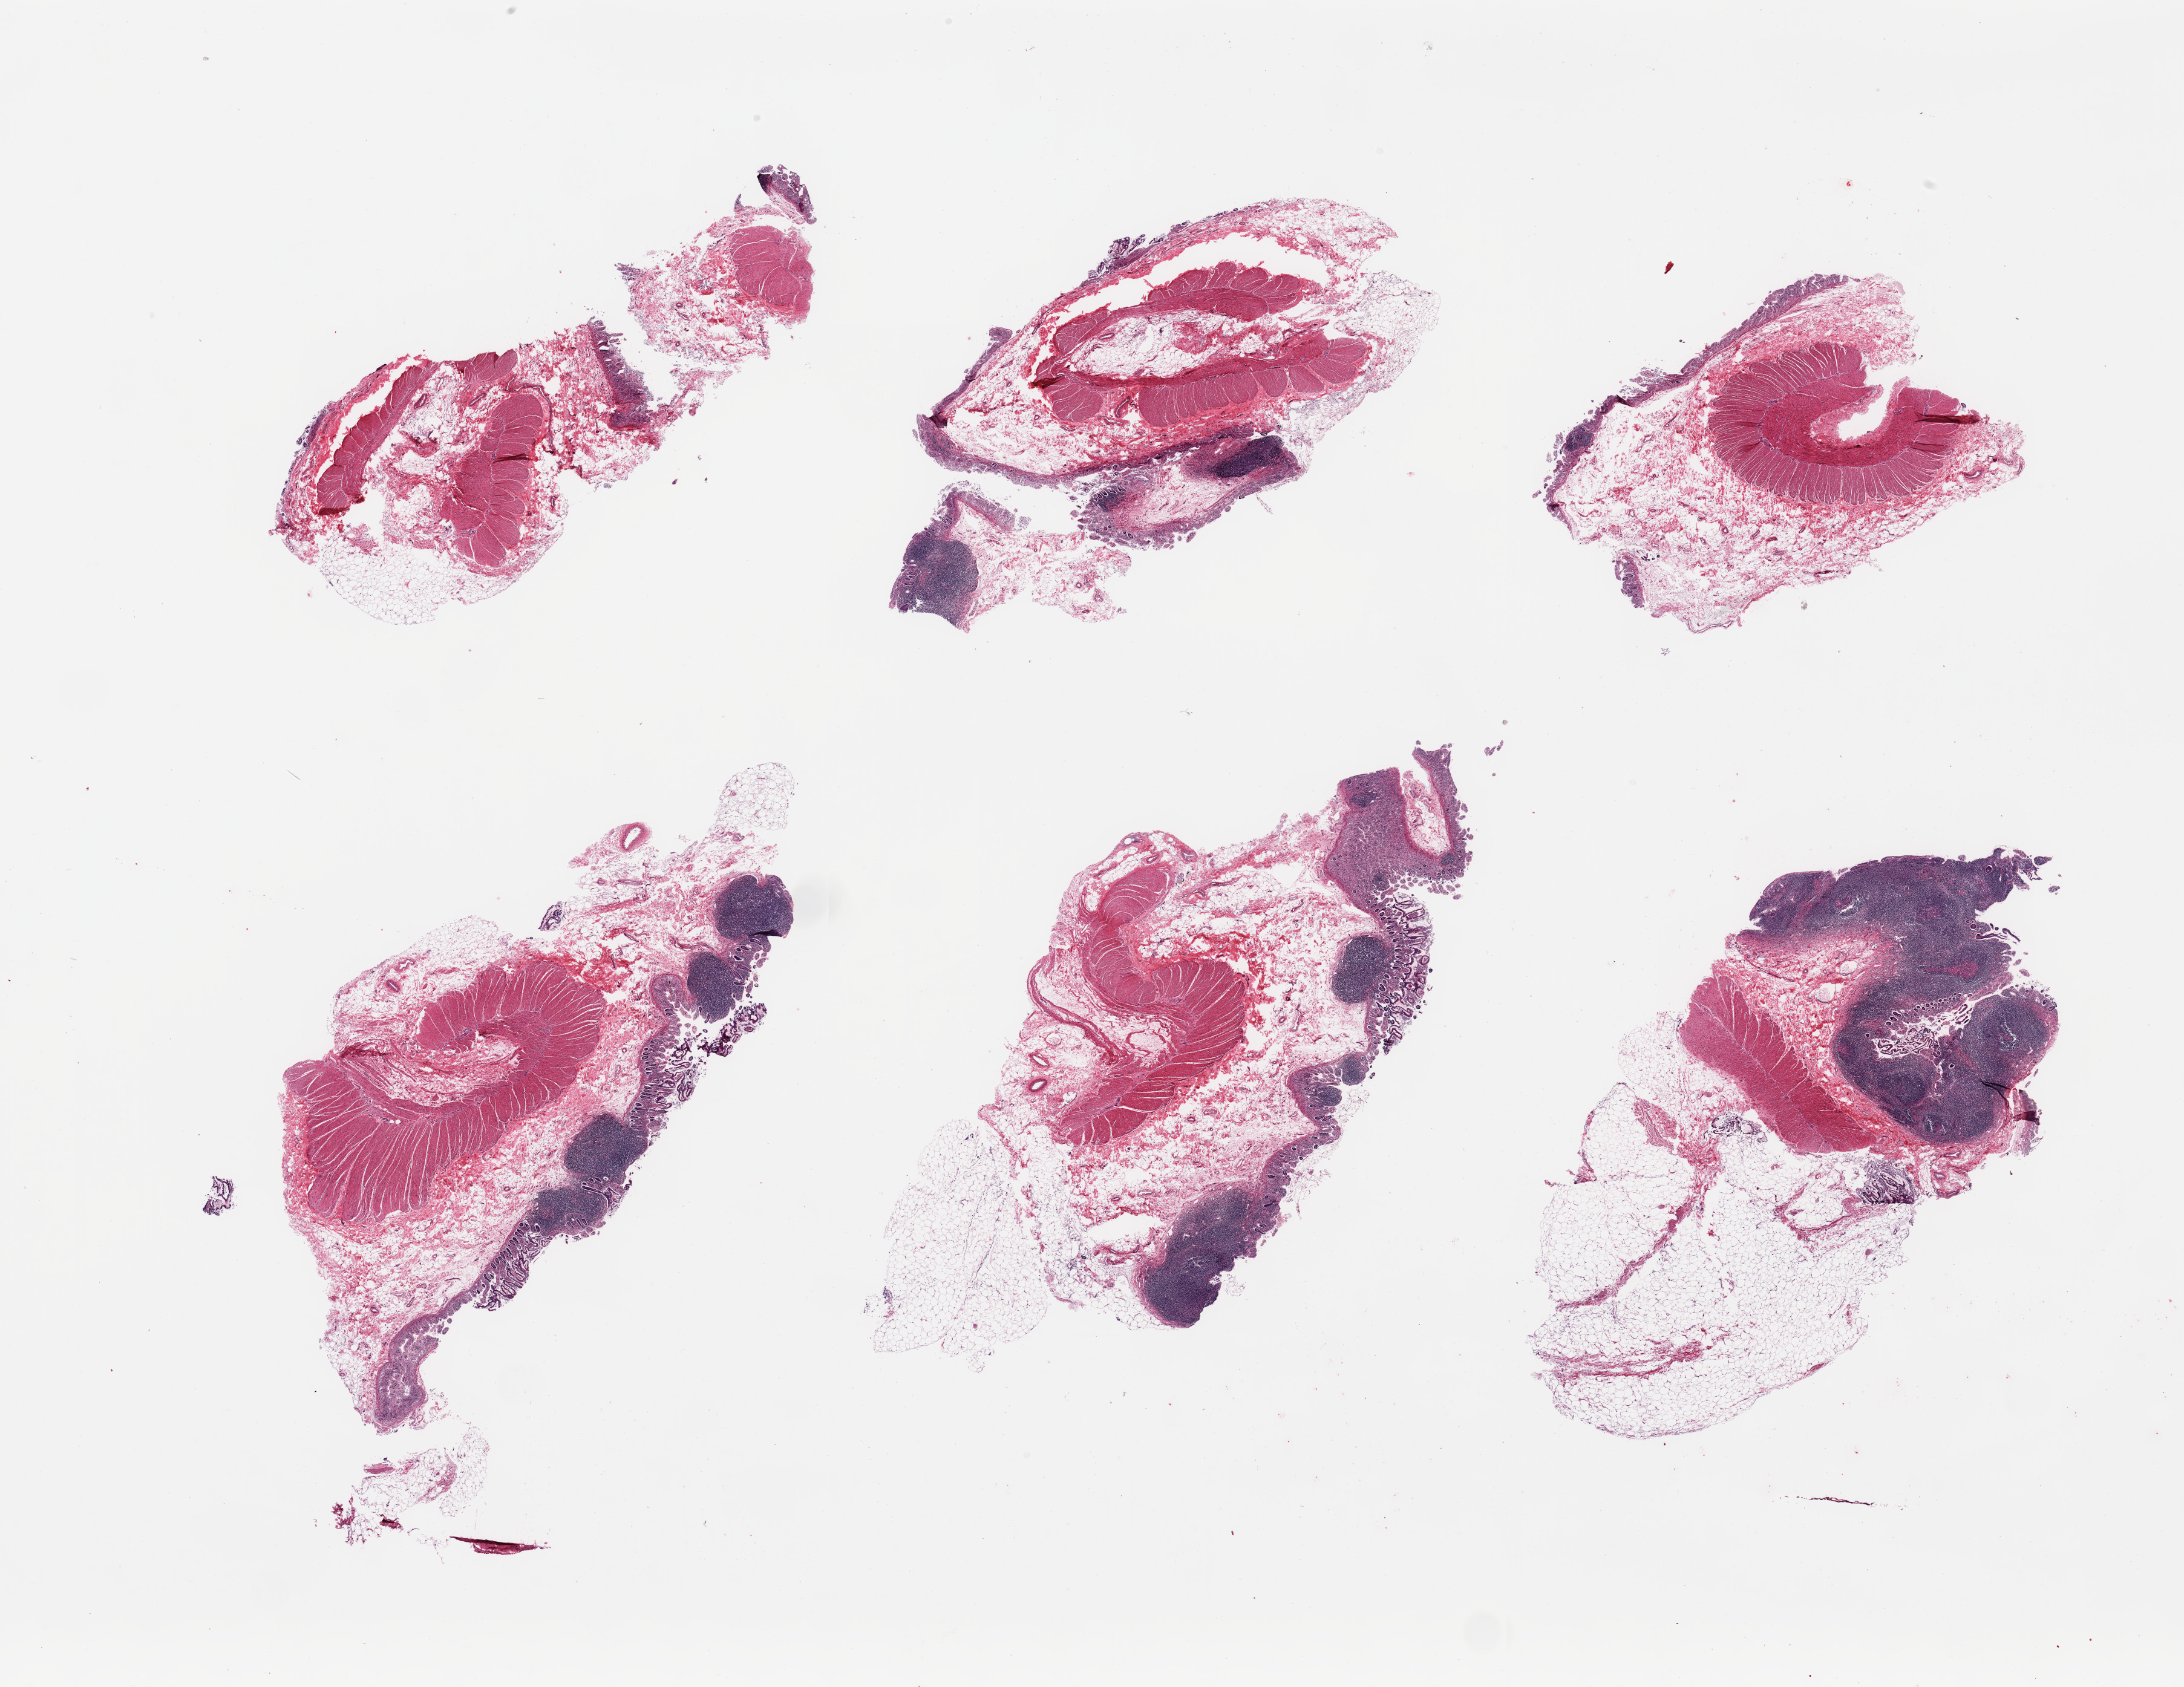
Digitized hematoxylin and eosin (H&E)-stained section — whole scanned area (about 28.5 x 22.1 mm) shown as a low-resolution overview. Donor sex: male.
• specimen: PAXgene-fixed paraffin-embedded (PFPE) section; target tissue: ileum; donor tissue sample